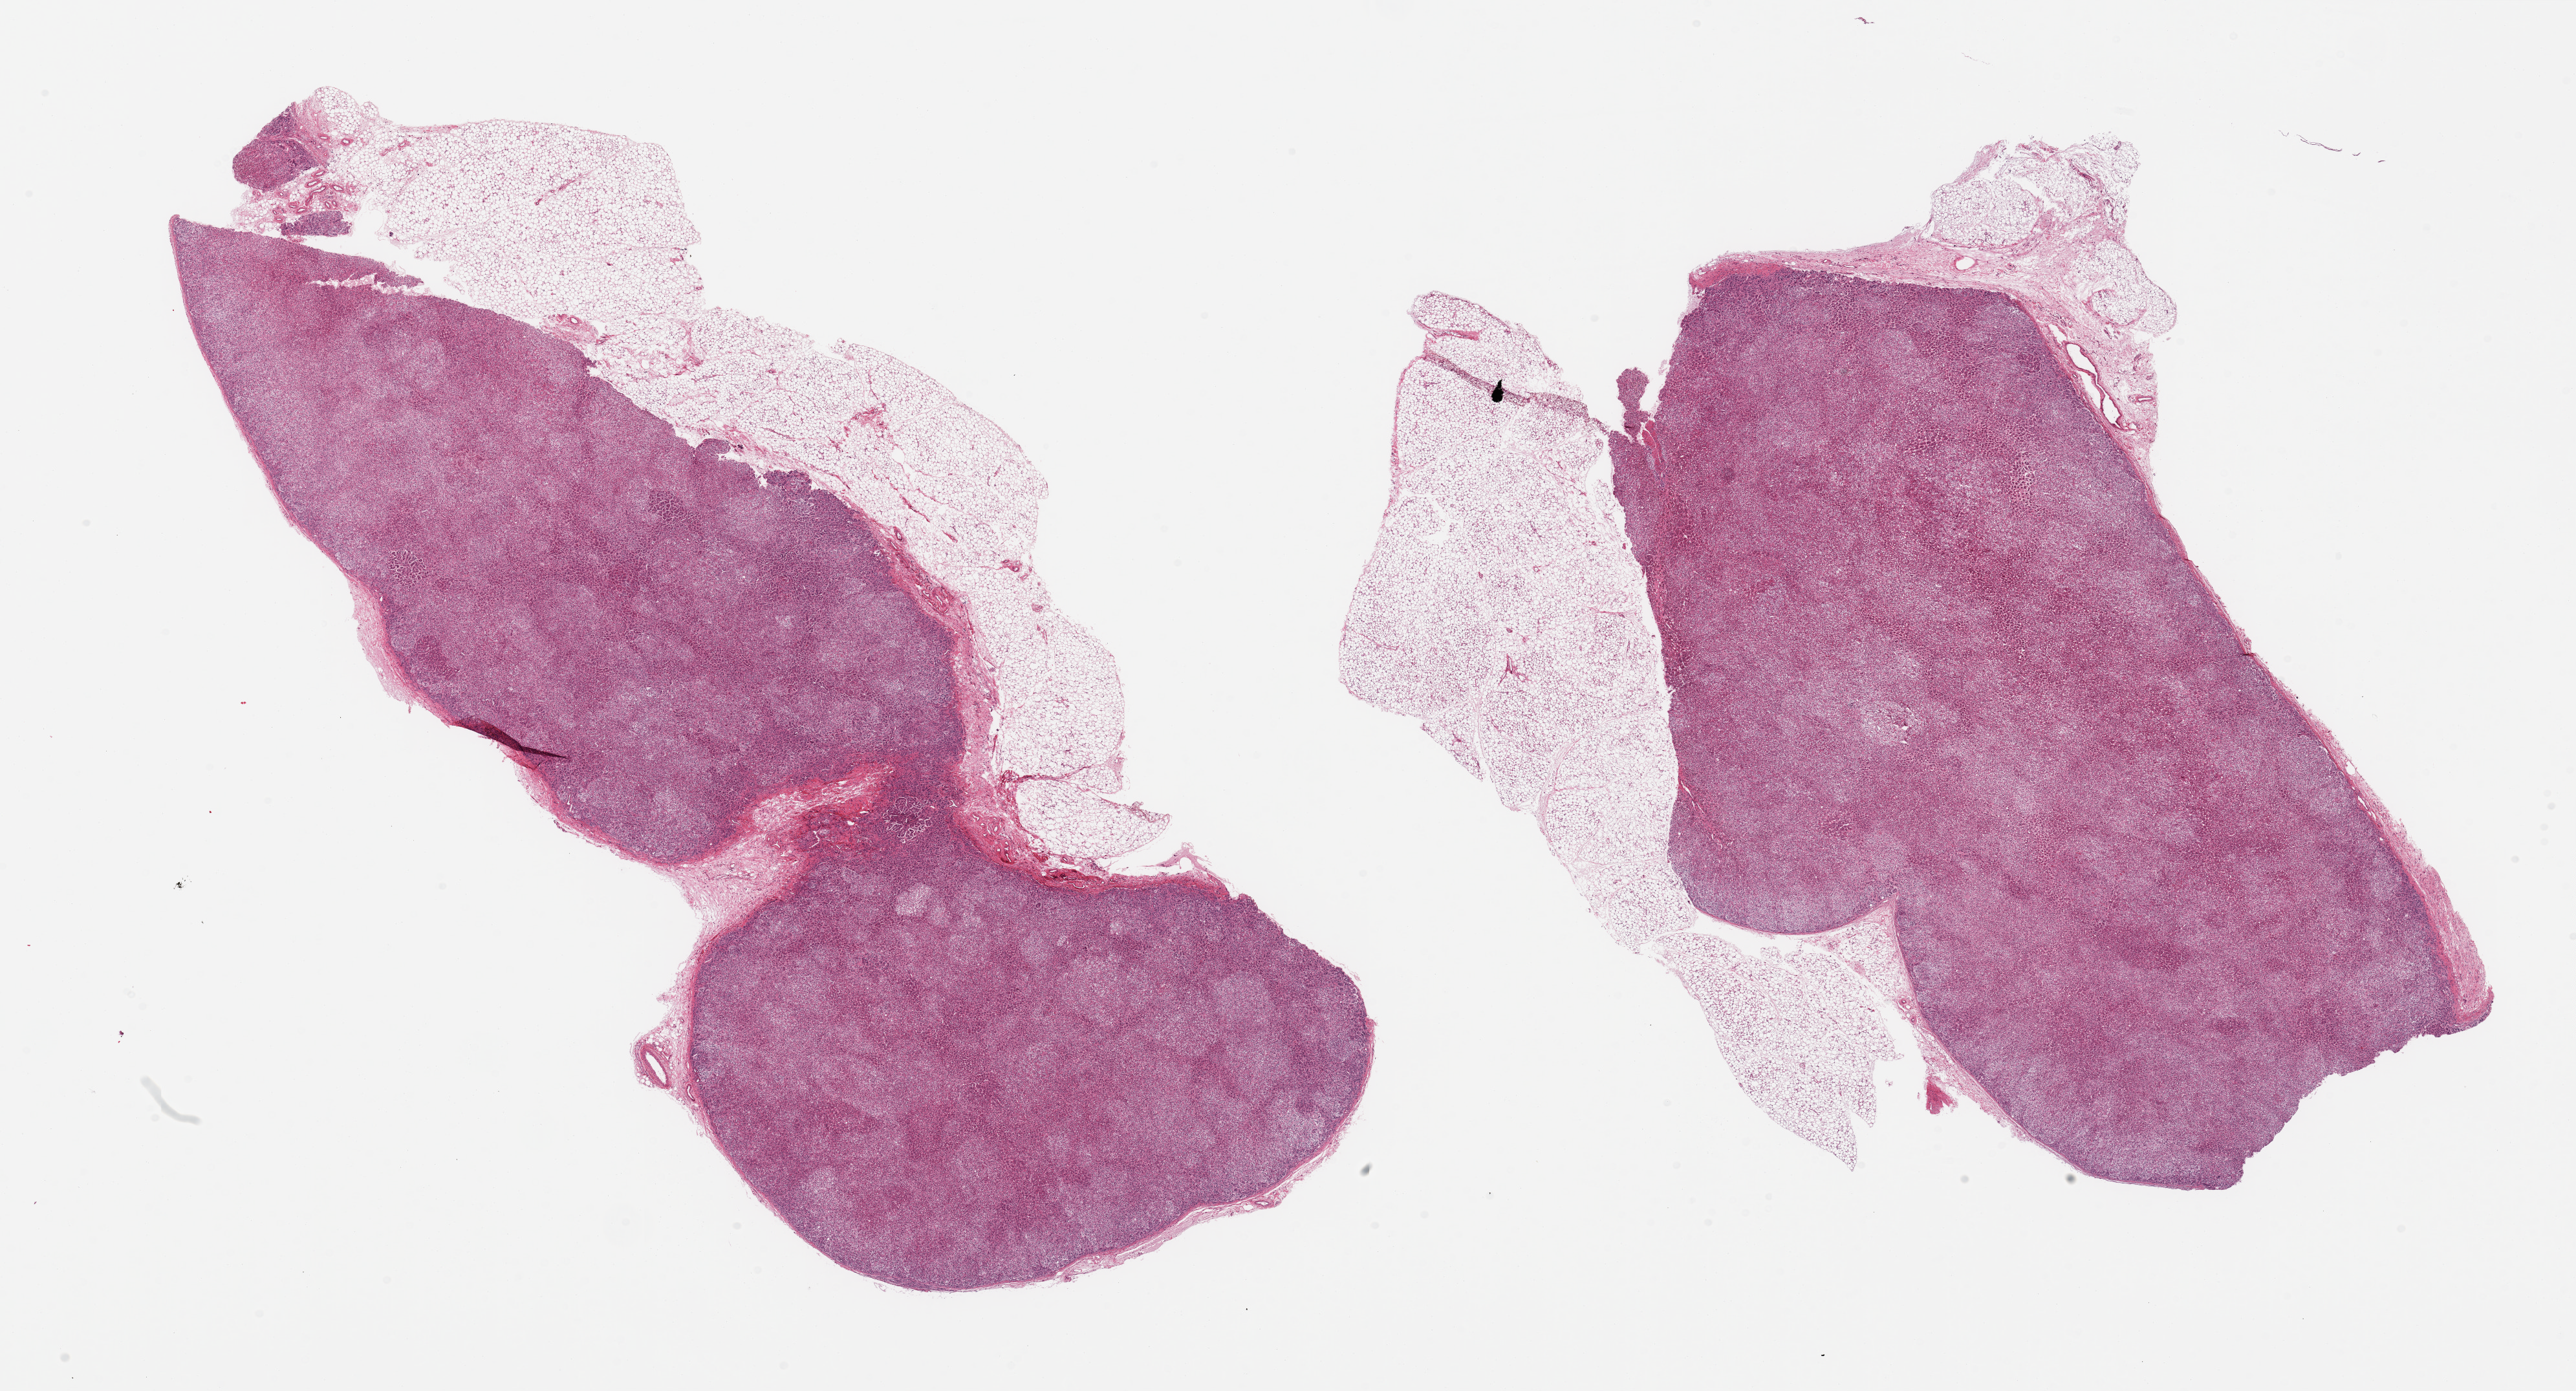
Whole-slide image, H&E stain, low-resolution overview of the scanned area, about 31.5 x 17.0 mm (slide scanned at 20x). PAXgene-fixed paraffin-embedded (PFPE) section. Section of adrenal gland (target tissue). Donor tissue sample.
Pathologist's review note for this sample: 2 pieces; up to 3.8 mm external untrimmed fat.